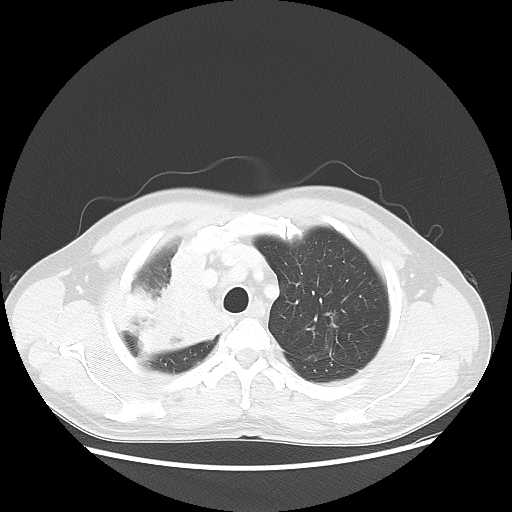
Chest CT, one axial slice. Position 44 of 56 along the scan axis. Reconstruction kernel LUNG. Lung window (W 1500 / L -600 HU). 5 mm slice thickness. 512 × 512 image matrix, field of view 398 × 398 mm. Male patient, age 60 years. From the clinical record (not read from this slice): clinical TNM (as recorded): T2a N1 M0.
Outlined on this slice (rectangle marked by the reading radiologist):
- lung tumour (recorded histology: squamous cell carcinoma): bounding box (x1, y1, x2, y2) in pixels: (129, 250, 230, 362)